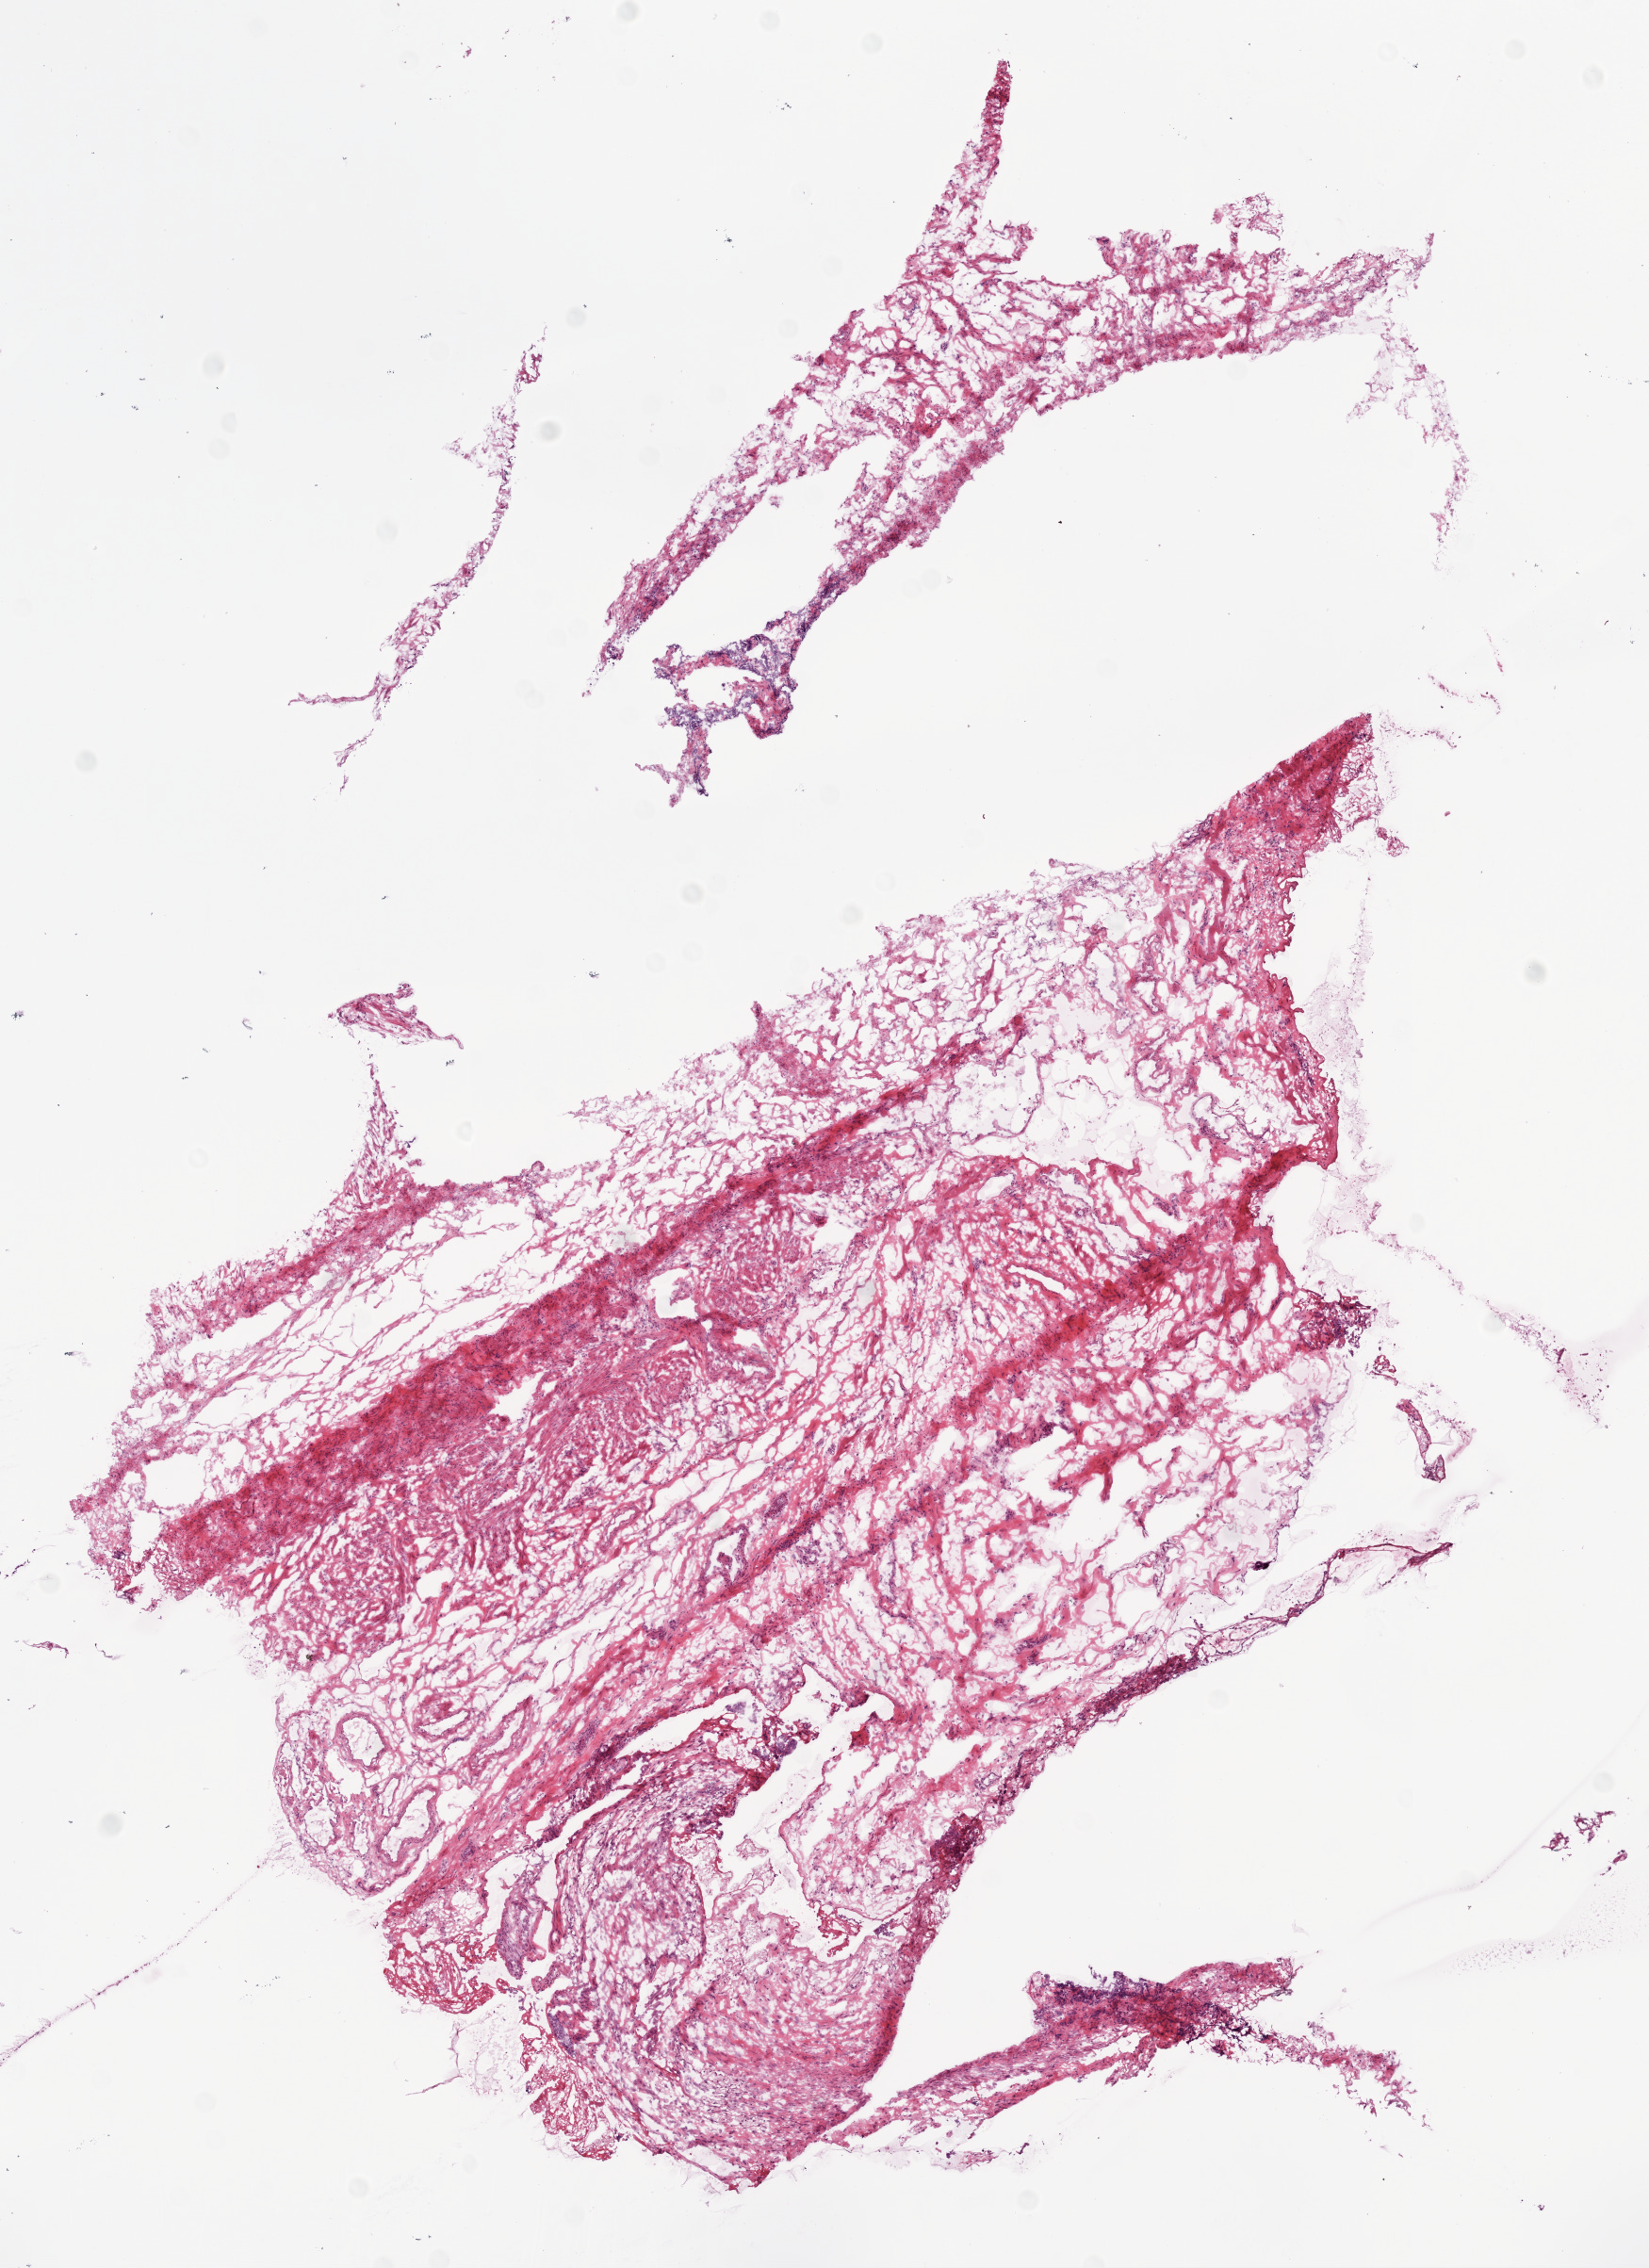
Digitized H&E-stained tissue section (whole slide) — whole scanned area (about 7.0 x 9.7 mm, slide scanned at 20x) shown as a low-resolution overview; frozen section from the bottom of the tissue portion; ovary, solid tissue normal (non-tumour tissue) sample. Patient: female, age at initial diagnosis 81 years.
• this section: solid tissue normal sample (biorepository sample class)
• patient diagnosis: Serous cystadenocarcinoma, NOS